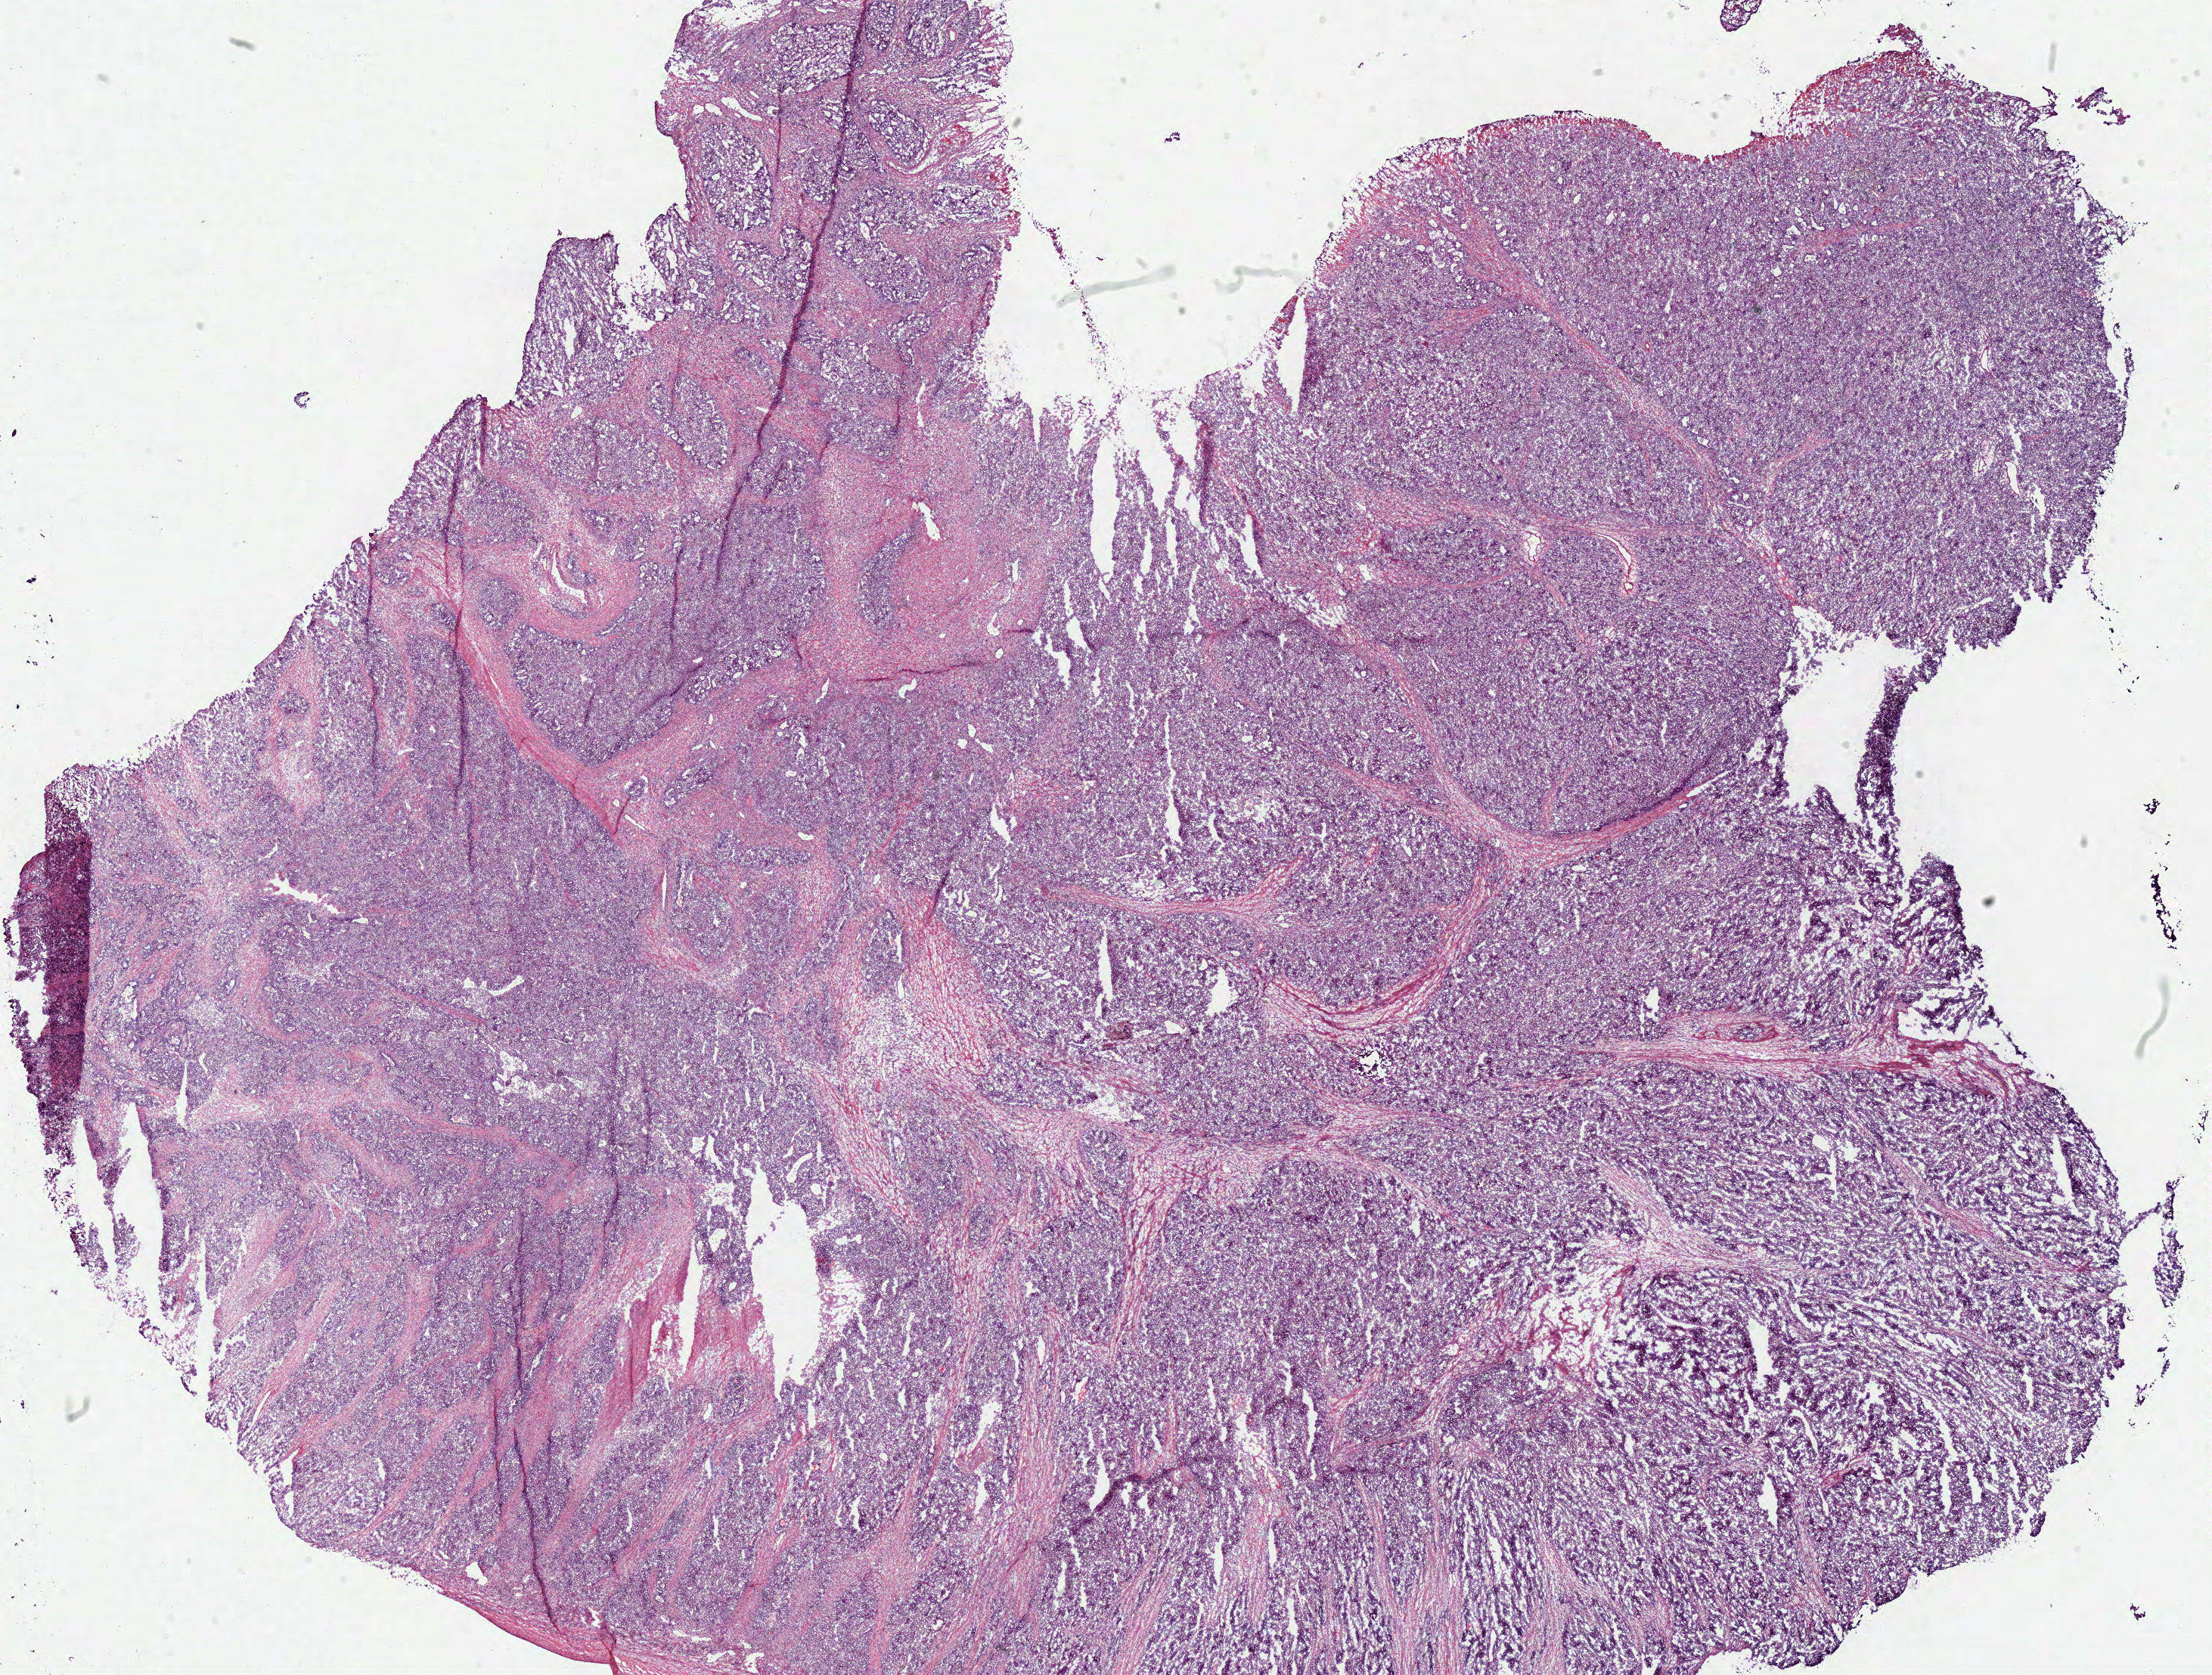
Digitized H&E tissue section (whole slide), low-resolution overview of the scanned area, about 23.0 x 17.4 mm (slide scanned at 40x); frozen section; primary tumour sample from the stomach. Male, age 75 years at initial diagnosis. Histologic grade: G3 (poorly differentiated). Composition of this section per pathologist review: tumour cells 80%, tumour nuclei 80%, normal cells 0%, stromal cells 10%, necrosis 10%.
- pathologic diagnosis: Adenocarcinoma, NOS
- AJCC pathologic stage: IIA (7th edition)